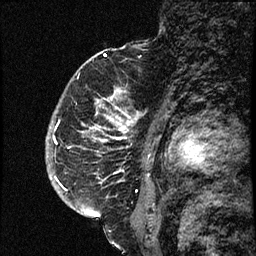
Breast MRI (dynamic contrast-enhanced), one sagittal slice; position 50 of 66 along the scan axis; dynamic contrast-enhanced study with each time point stored as its own series, time point 2 of 3 at this slice position (early post-contrast, ordered by acquisition time); 1.5 T; TE 4.2 ms, TR 17.6 ms; 2 mm slice thickness; 256 × 256 image matrix, field of view 200 × 200 mm. Female patient. From the clinical record (not read from this slice): setting: breast cancer imaged before/during neoadjuvant chemotherapy; receptor status: HER2-positive.
Outlined on this slice (semi-automatic segmentation, software-assisted and operator-edited):
- analysis volume of interest (the breast-tissue region the enhancement analysis was run in; not a lesion): box from (x=52, y=69) to (x=139, y=209) px
- tumour enhancement mask (voxels above the 100 % enhancement threshold inside the analysis volume of interest): (x=53, y=98)–(x=137, y=191)